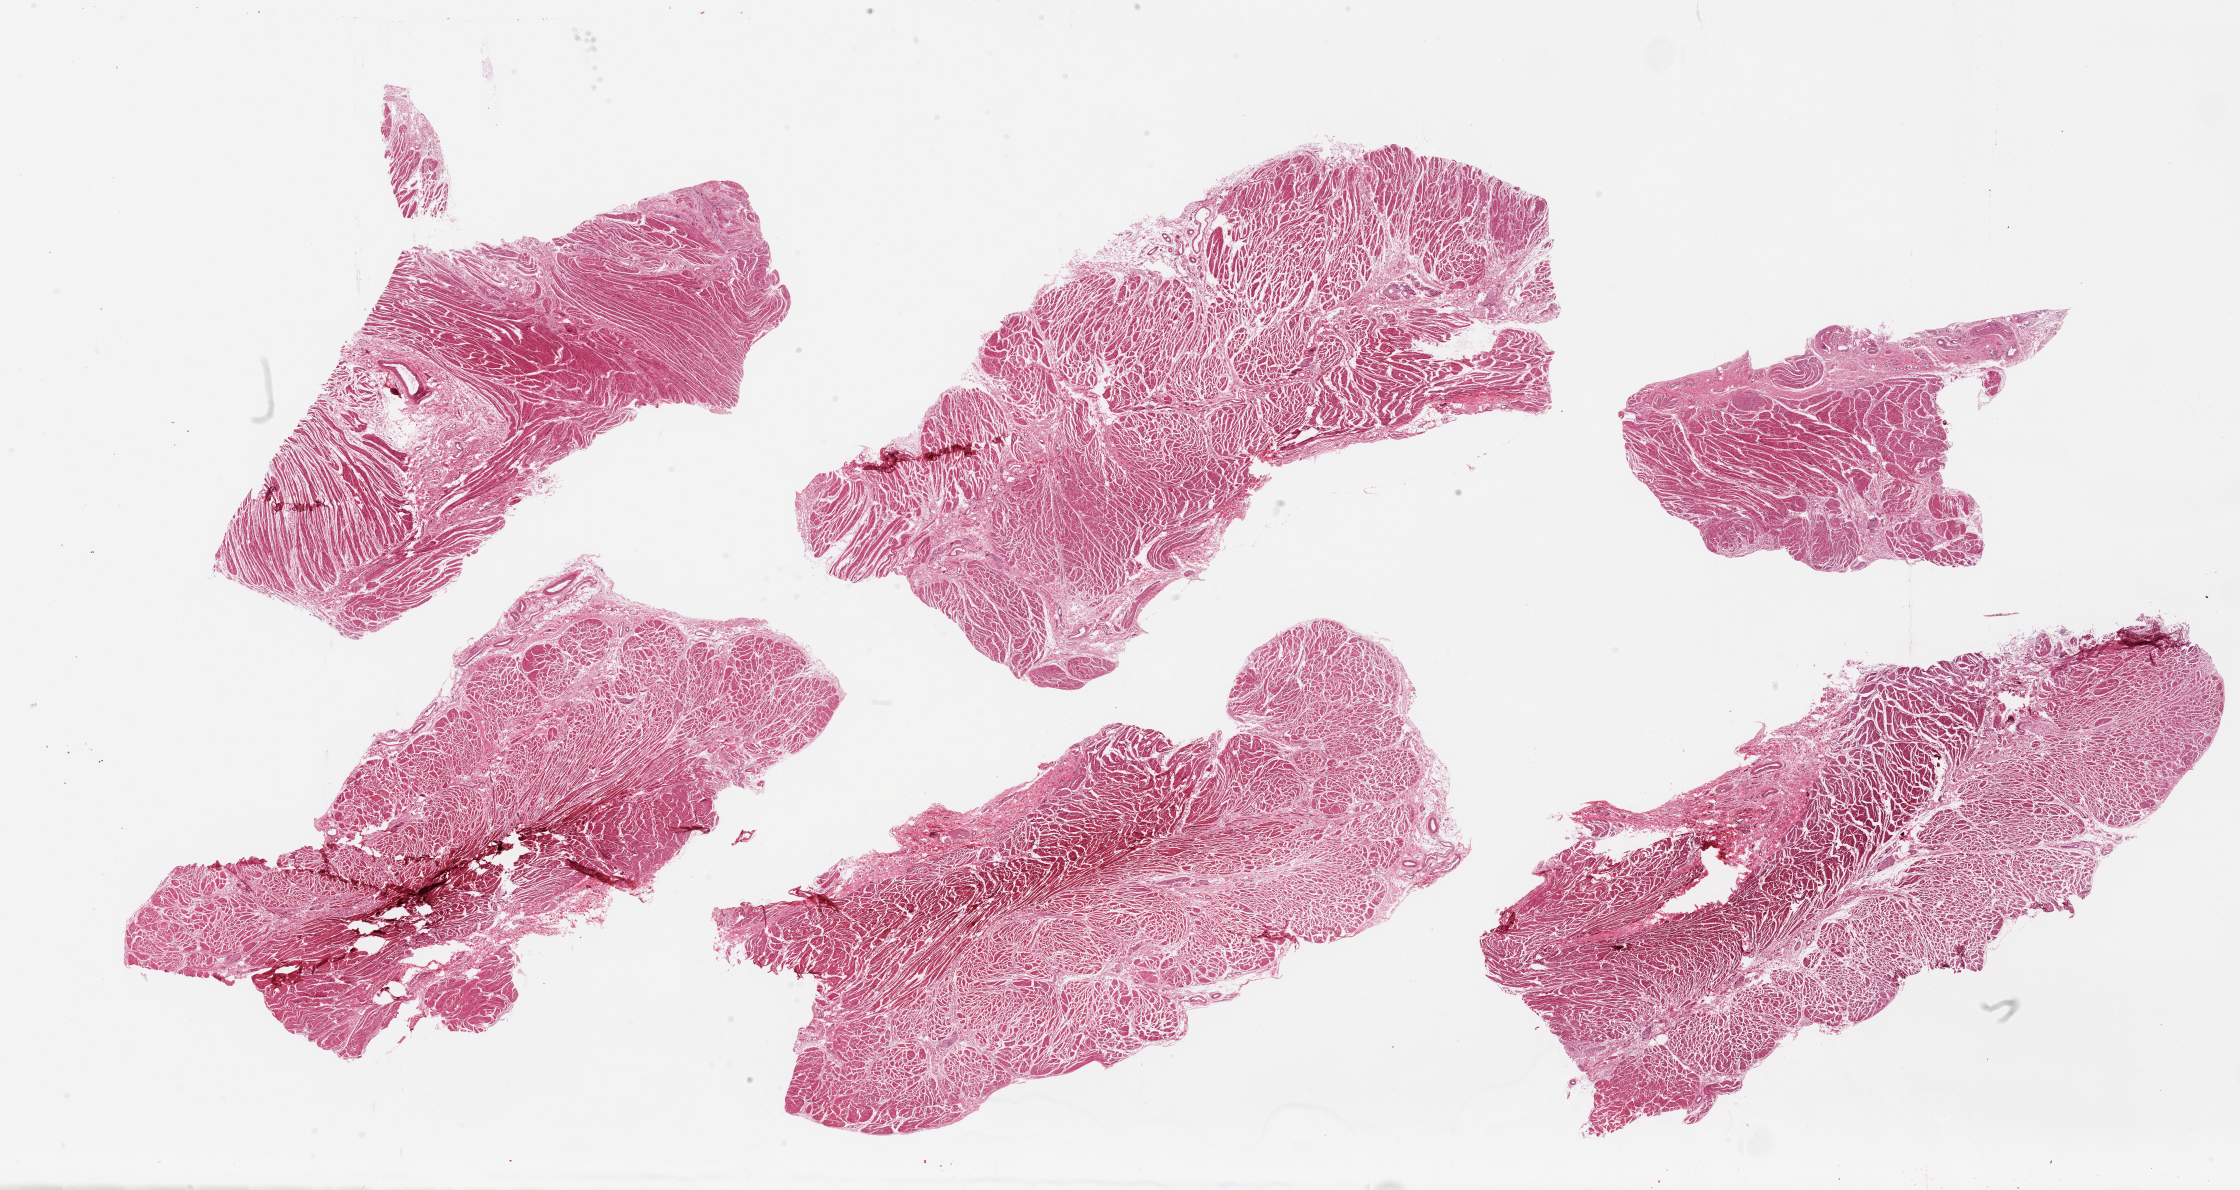
Digitized H&E-stained section, brightfield — low-resolution overview of the scanned area, about 35.4 x 18.8 mm (acquisition: 20x scan), PAXgene-fixed paraffin-embedded (PFPE) section, sampled site (target tissue): gastroesophageal junction, donor tissue sample. Donor sex: male.
Review note (as recorded): 6 pieces.